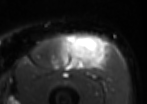
MRI of an extremity soft-tissue mass, one axial slice; position 41 of 85 along the scan axis; T2-weighted fat-saturated; MR volume resampled by the dataset authors to the PET/CT grid (not the native acquisition matrix); 147 × 104 image matrix. Male patient. Case-level facts recorded for this patient, not image findings: histological type: extraskeletal osteosarcoma; grade: high; site of the primary tumour: thigh.
Annotated regions visible in this slice (expert contour drawn on MRI and transferred to this co-registered scan by the dataset authors):
- gross tumour volume (mass): box from (x=60, y=35) to (x=102, y=70) px